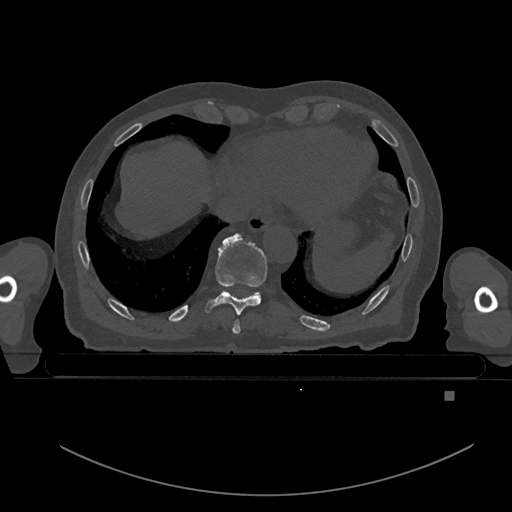
CT including the spine, one axial slice. Position 141 of 969 along the scan axis. Bone window (W 1800 / L 400 HU). 512 × 512 image matrix, field of view 456 × 456 mm. Male patient, age 82 years. From the clinical record (not read from this slice): primary cancer: prostate.
Structures marked on this image (semi-automatically segmented with operator editing):
- T8 vertebra: bounding box <232,319,241,334> (left, top, right, bottom; pixels)
- T9 vertebra: <205,233,267,315>